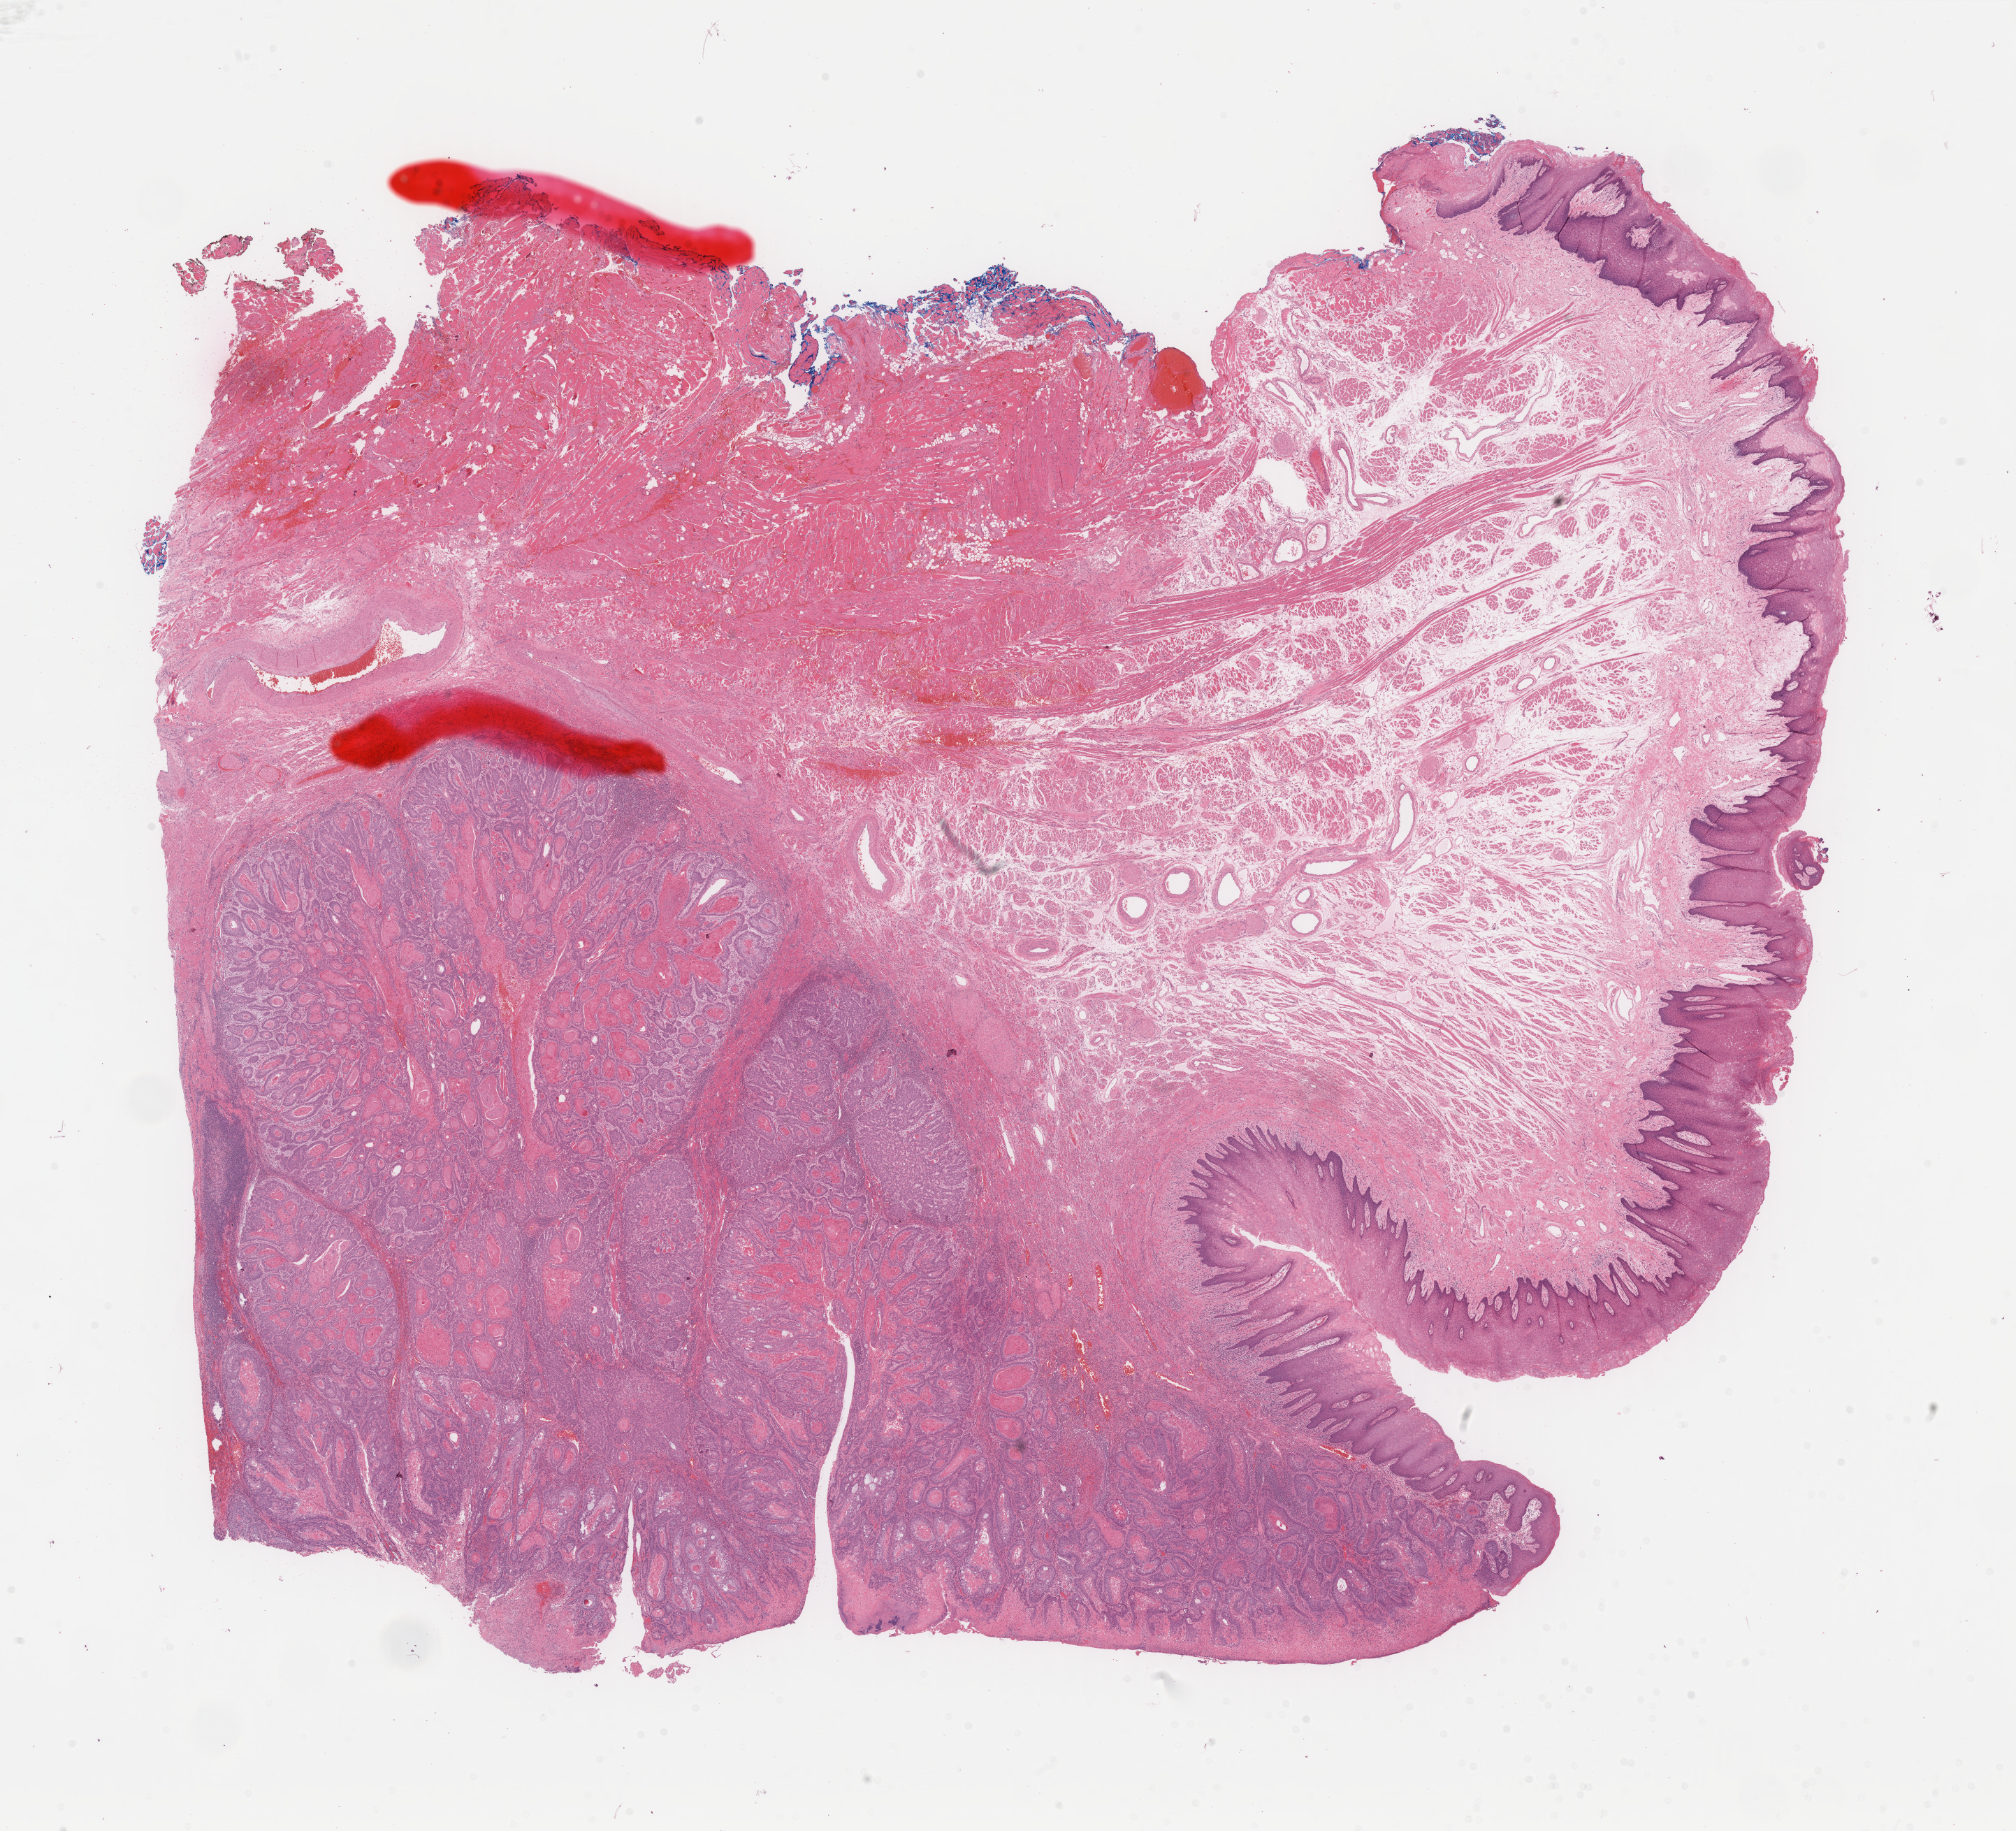
Whole-slide histology image, Hematoxylin and eosin (H&E) stained, whole scanned area (about 22.8 x 20.7 mm, slide scanned at 40x) shown as a low-resolution overview, formalin-fixed paraffin-embedded (FFPE) diagnostic section, primary tumour sample from the head and neck. Female patient; age at initial diagnosis 70 years. Histologic grade: G2 (moderately differentiated).
Laterality: right. TNM: T2 N0 M0. Diagnosis: Squamous cell carcinoma, keratinizing, NOS (tongue, NOS). AJCC pathologic stage: II.